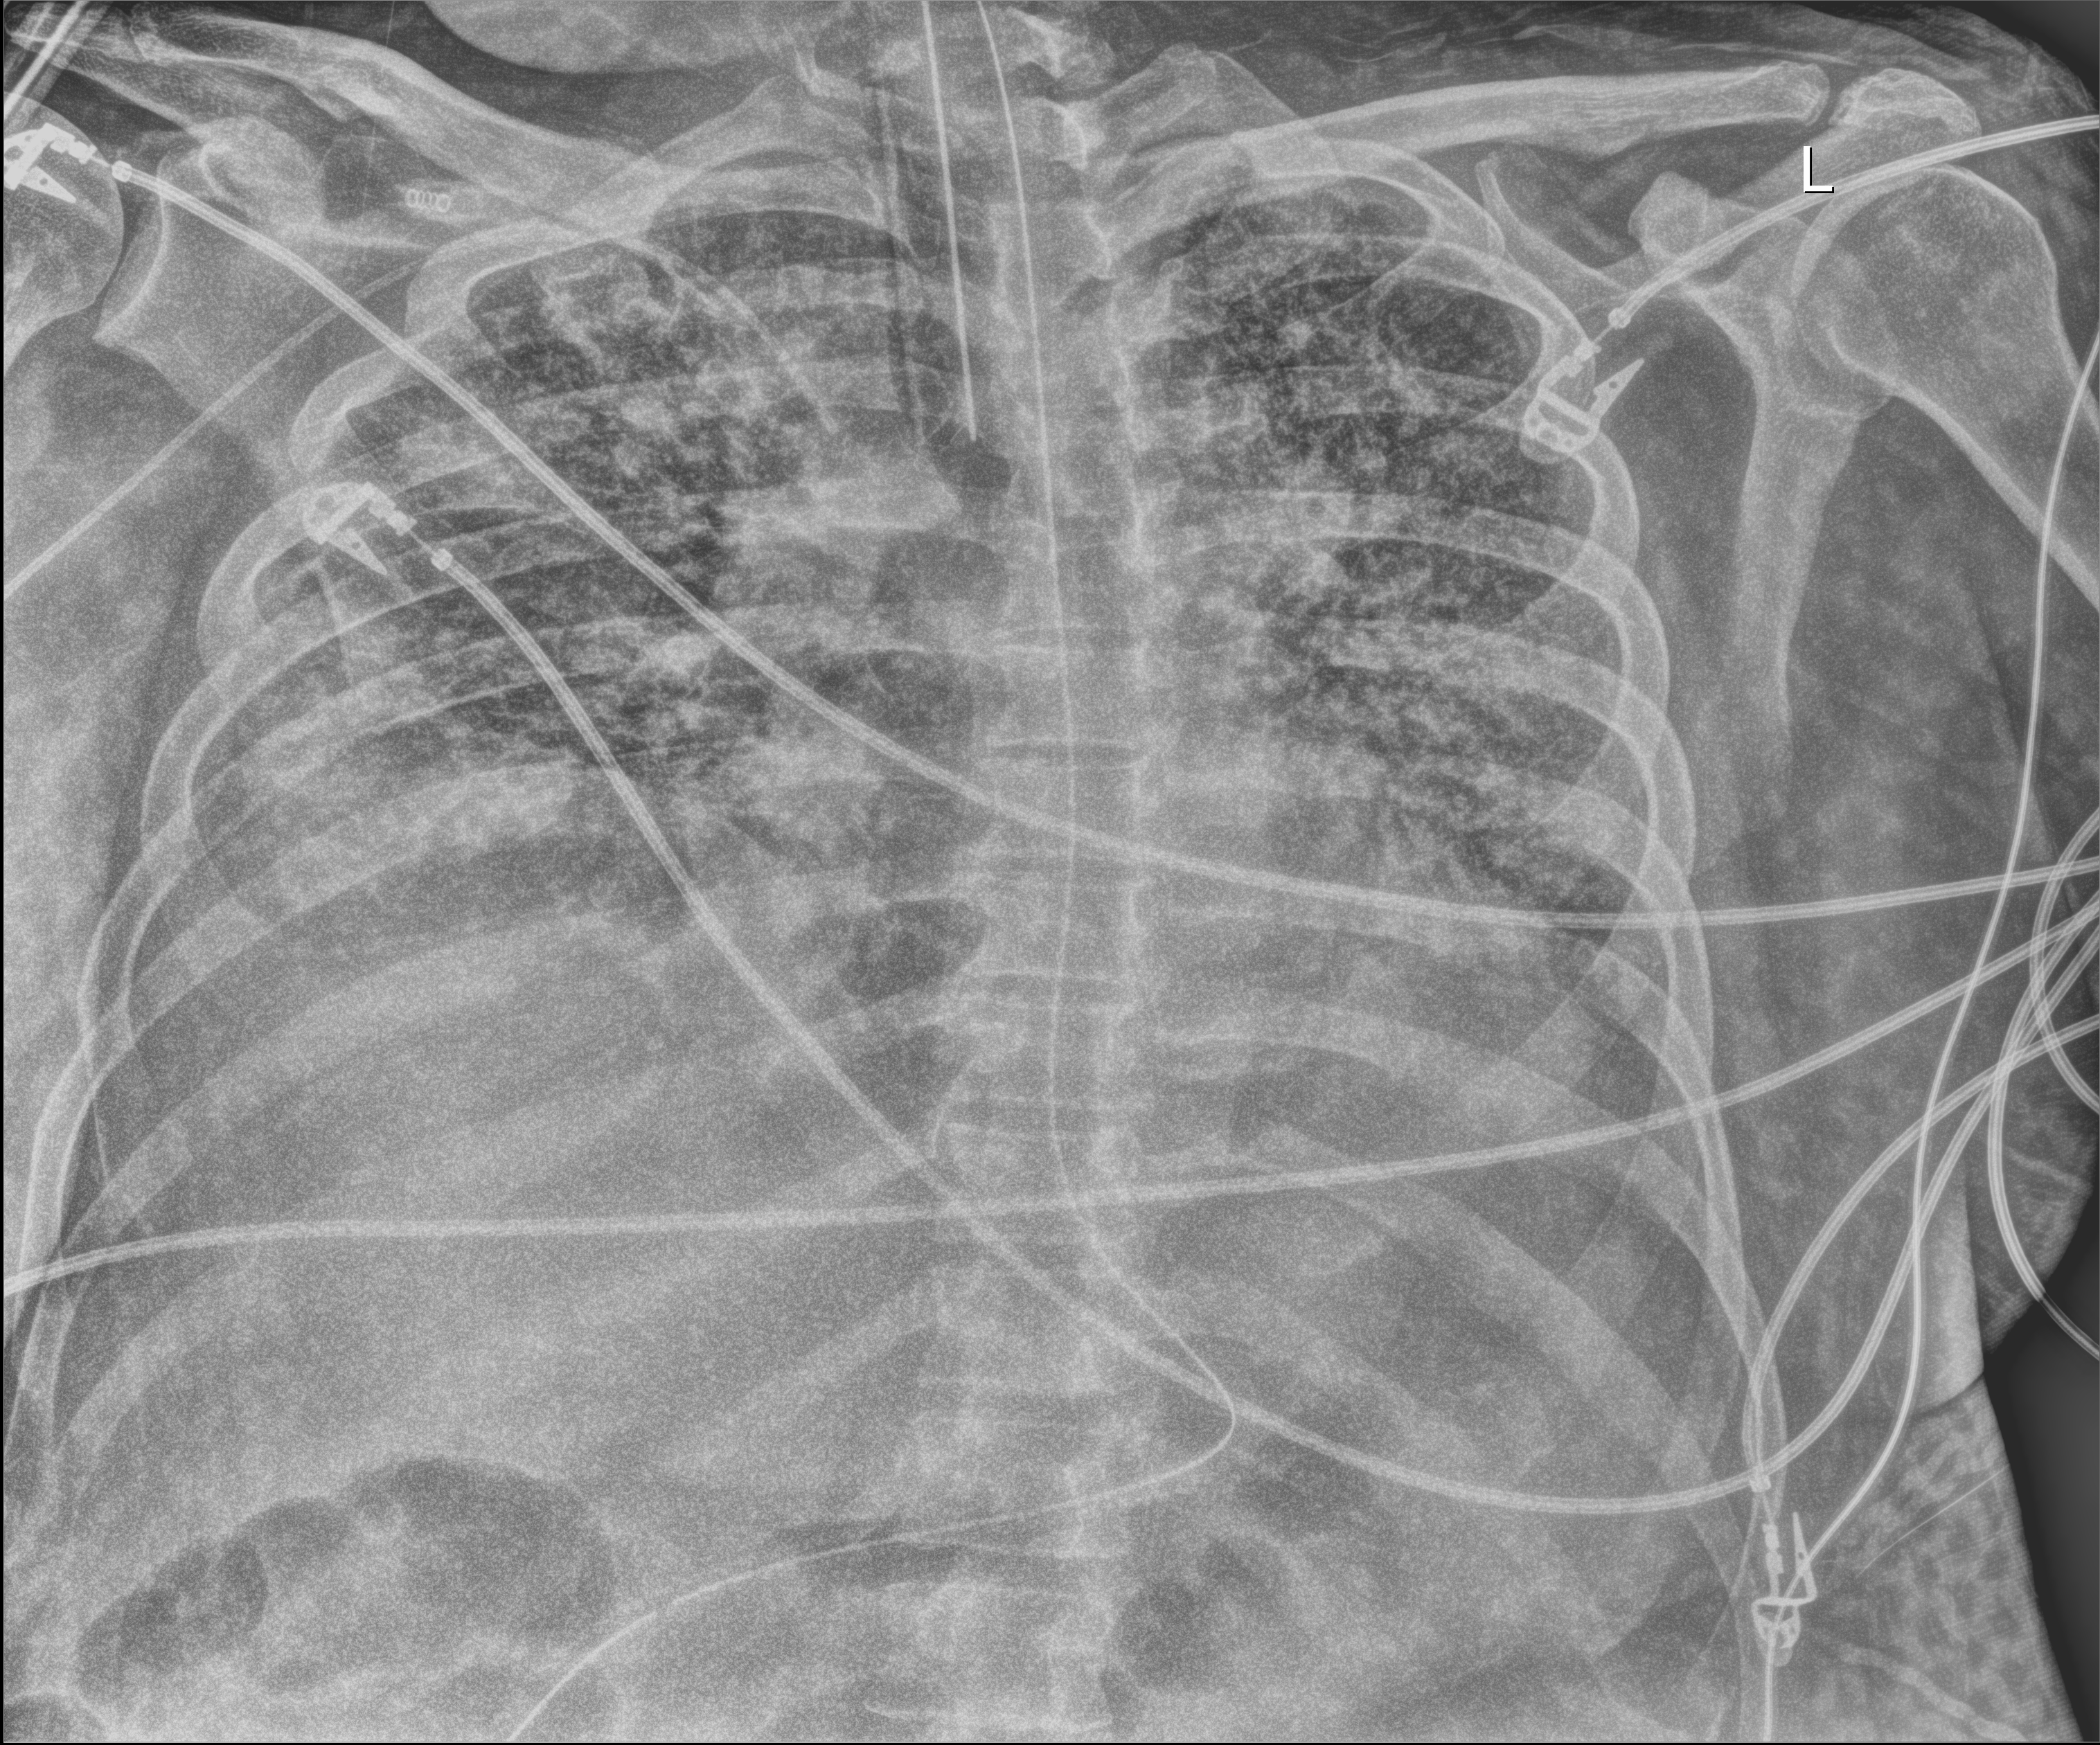
Portable chest radiograph; anteroposterior (AP) projection. Male patient hospitalised with COVID-19, age 18–59 years.
Admission-level facts for this patient (not findings on this image; timing relative to this image not recorded):
- admitted to intensive care during this hospital stay: yes
- COPD (admission record): no